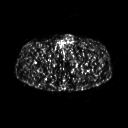
FDG PET of an extremity soft-tissue mass (from a PET/CT study), one axial slice. Slice 266 of 267 in the series (ordered by position). 3.27 mm slice thickness. 128 × 128 image matrix, field of view 500 × 500 mm. Patient: male, 27 years. From the clinical record (not read from this slice): histological type: extraskeletal osteosarcoma; grade: high; site of the primary tumour: left adductur.
Outlined on this slice (expert contour drawn on MRI and transferred to this co-registered scan by the dataset authors):
- gross tumour volume (mass): bounding box (x1, y1, x2, y2) in pixels: (73, 49, 97, 74)